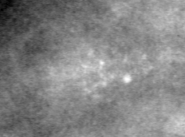
Region of interest cut from a scanned film mammogram (one marked finding), left breast, CC view.
Calcifications, morphology pleomorphic, distribution clustered; BI-RADS assessment category 4; subtlety rating 2 on a 1 (subtle) to 5 (obvious) scale; pathology (as recorded): benign.